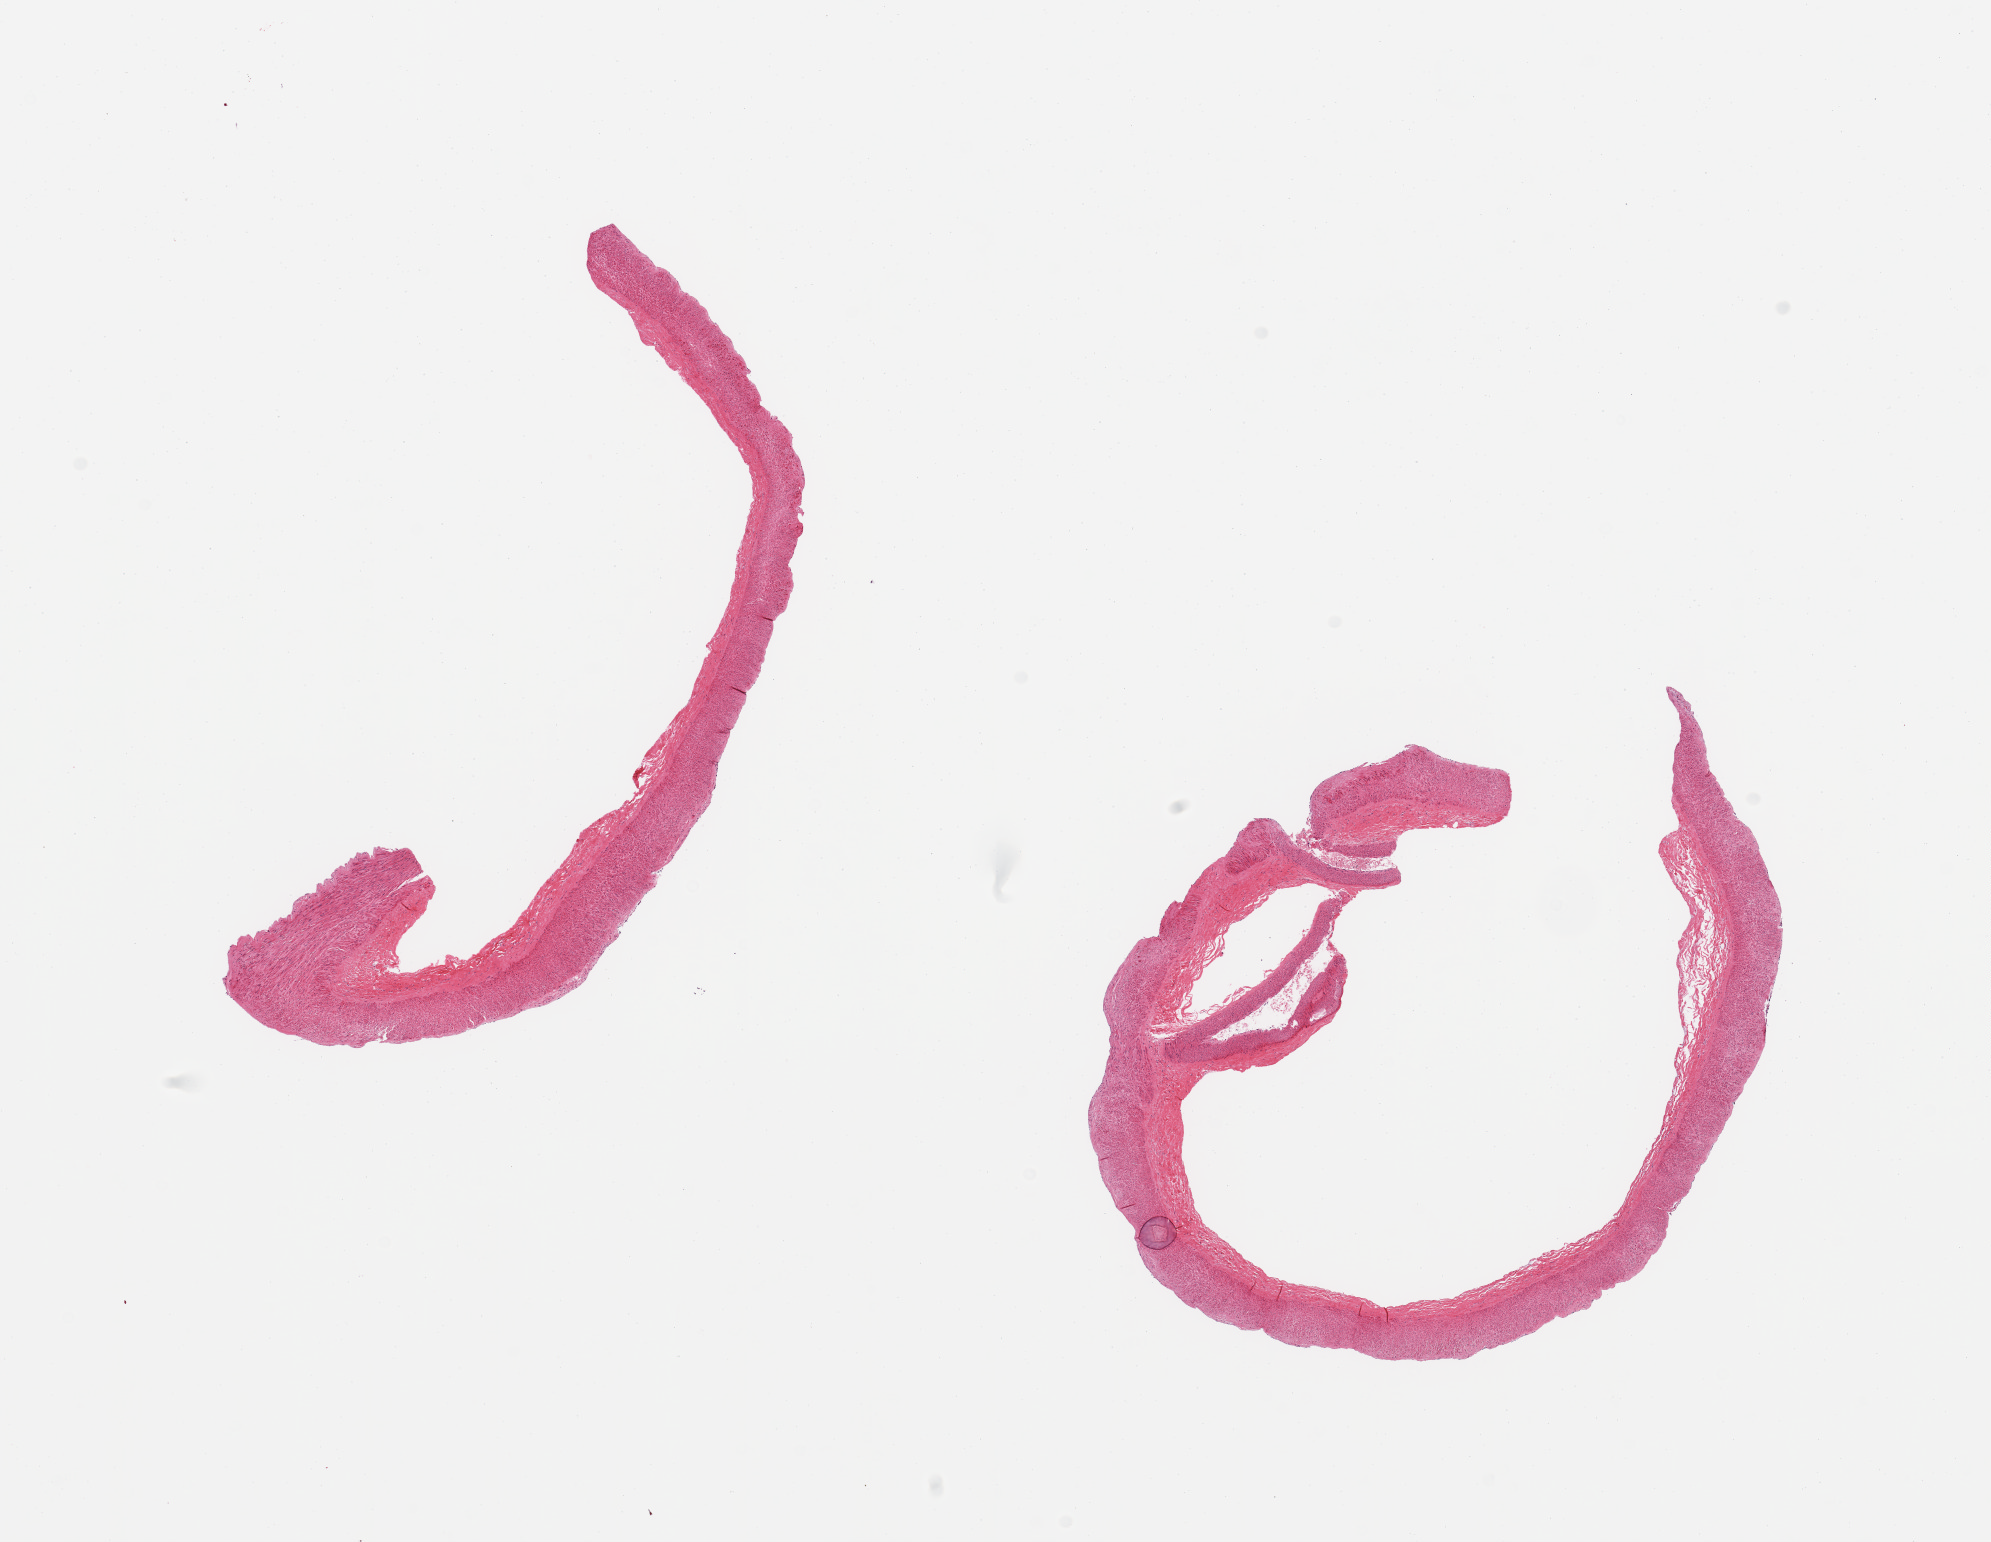
Whole-slide image, haematoxylin and eosin stain — low-resolution overview of the scanned area, about 15.8 x 12.2 mm (slide scanned at 20x), PAXgene-fixed, paraffin-embedded tissue, sampled site (target tissue): tibial artery, tissue donor sample. Donor: male.
• pathologist's review note for this sample: 2 pieces; minimal plaque; well trimmed